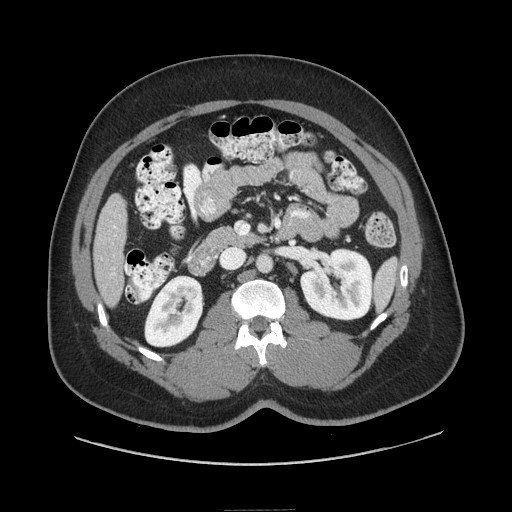
Contrast-enhanced abdominal CT (liver protocol), one axial slice. Position 22 of 87 along the scan axis. Reconstruction kernel STANDARD. Soft-tissue window (W 400 / L 40 HU). 2.5 mm slice thickness. 512 × 512 image matrix. From the clinical record (not read from this slice): diagnosis: hepatocellular carcinoma (patient treated with transarterial chemoembolisation; whether this scan precedes or follows treatment is not stated here); TNM stage (as recorded): Stage-II; Child-Pugh class: A; tumour differentiation: moderately differentiated.
Annotated regions visible in this slice (semi-automatic segmentation, software-assisted and operator-edited):
- liver parenchyma outside the tumour (the mass and vessels are separate outlines, so this box may not span the whole liver): bounding box <94,194,126,306> (left, top, right, bottom; pixels)
- liver vessels: <112,225,116,275>